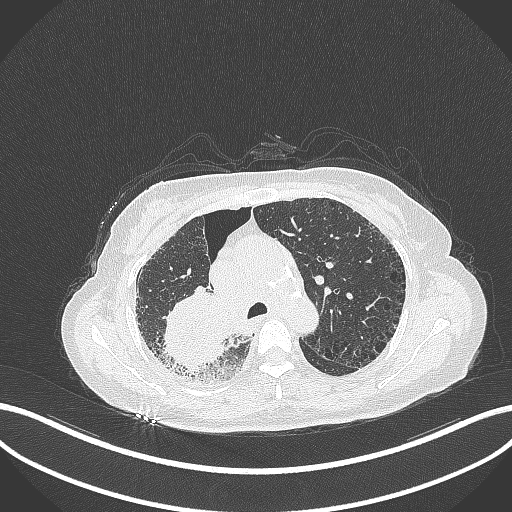
Chest CT, one axial slice; slice 237 of 408 in the series (ordered by position); reconstruction kernel B70f; lung window (W 1500 / L -600 HU); 1 mm slice thickness; 512 × 512 image matrix, field of view 400 × 400 mm. Female patient, age 64 years. Case-level facts recorded for this patient, not image findings: clinical TNM (as recorded): T3 N3 M0.
Annotated regions visible in this slice (rectangle marked by the reading radiologist):
- lung tumour (recorded histology: squamous cell carcinoma): bounding box [x1, y1, x2, y2] px = [158, 284, 230, 375]